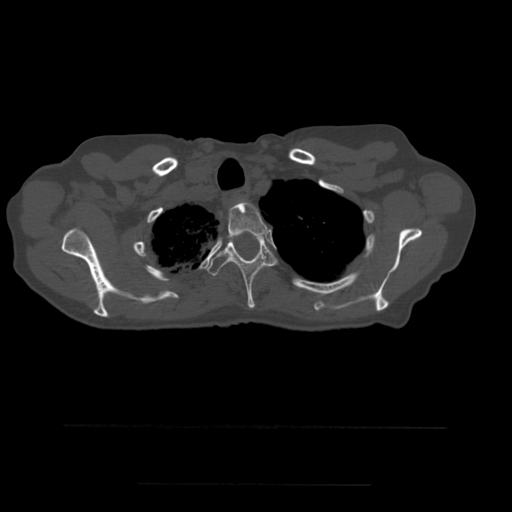
CT including the spine, one axial slice; slice 426 of 544 in the series (ordered by position); bone window (W 1800 / L 400 HU); 512 × 512 image matrix. Patient age 58 years. From the clinical record (not read from this slice): primary cancer: lung.
Outlined on this slice (semi-automatic segmentation, software-assisted and operator-edited):
- T2 vertebra: bounding box (x1, y1, x2, y2) in pixels: (228, 202, 268, 240)
- T3 vertebra: (207, 235, 277, 309)